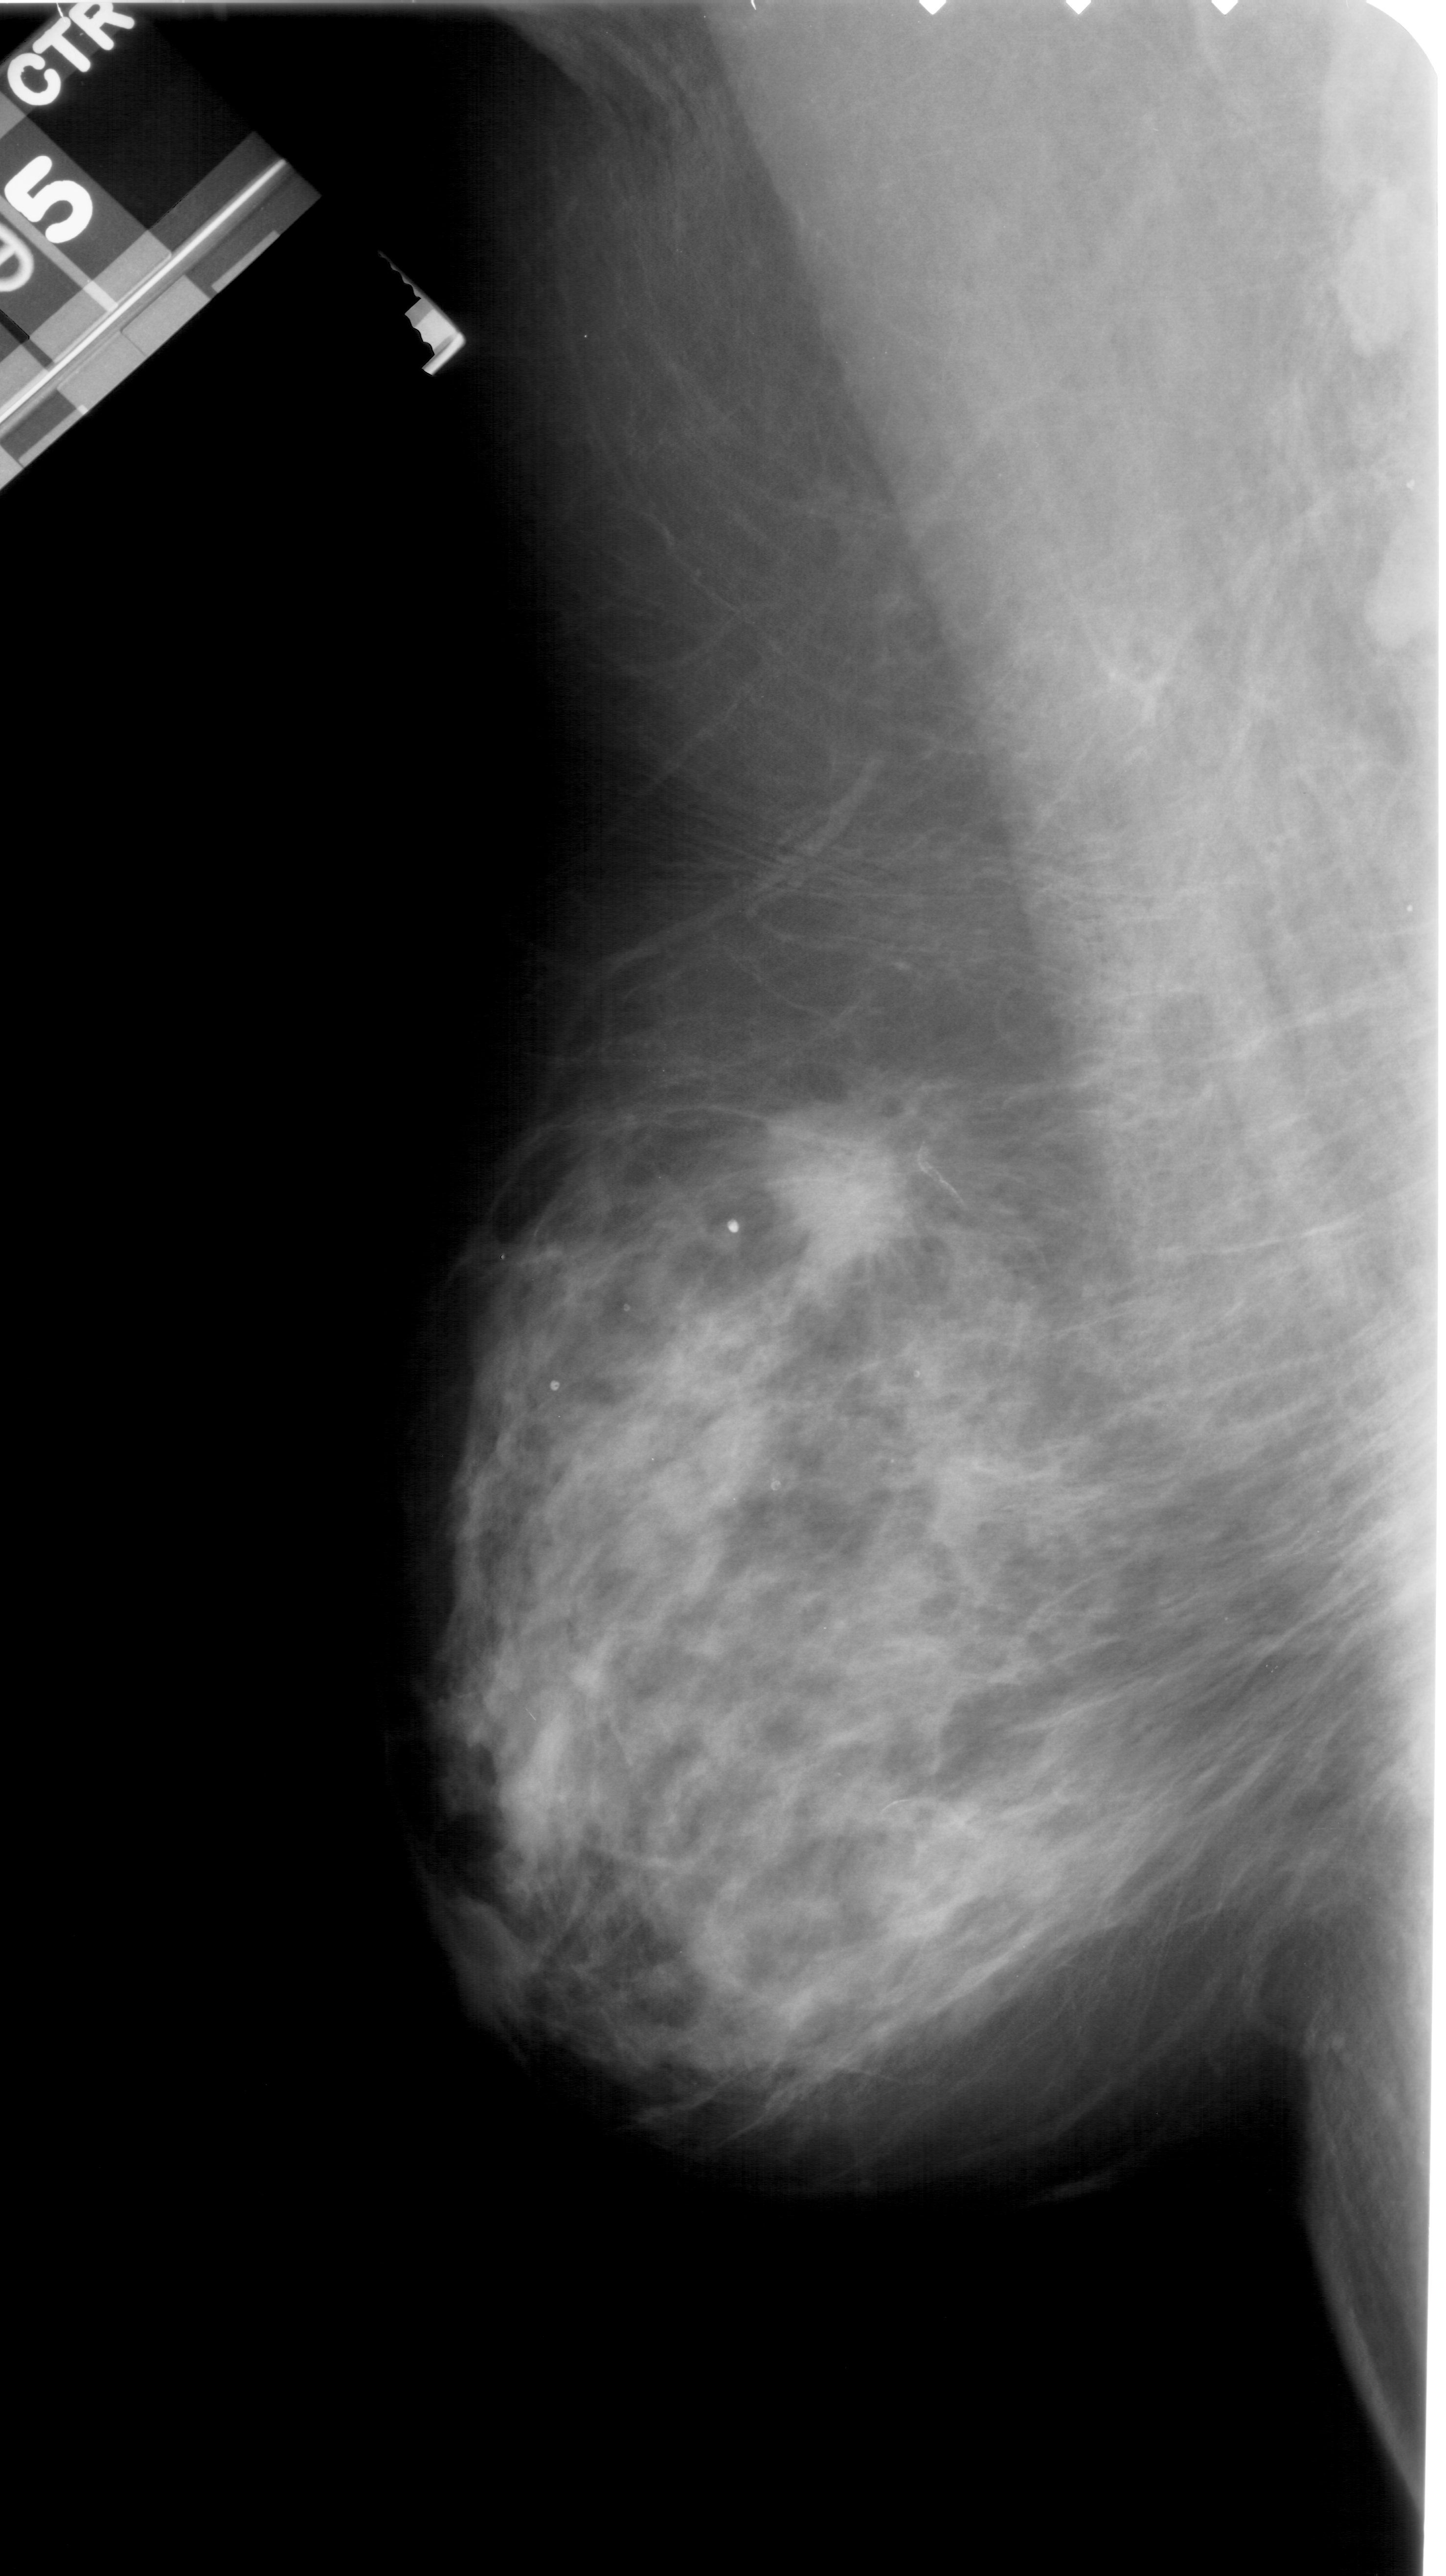
Mammogram (digitized film); left breast; mediolateral oblique (MLO) view; 1446 × 2576 image matrix.
Expert-marked regions of interest on this film, with their recorded descriptors:
- mass, shape irregular, margins spiculated; BI-RADS assessment category 5; subtlety rating 5 on a 1 (subtle) to 5 (obvious) scale; pathology (as recorded): malignant: box from (x=741, y=1093) to (x=972, y=1297) px